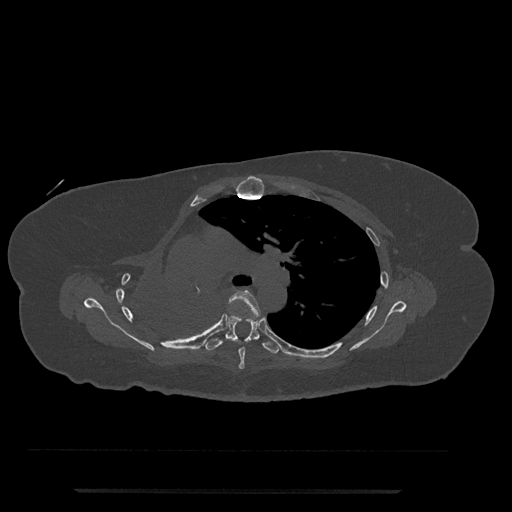
CT including the spine, one axial slice; position 516 of 797 along the scan axis; reconstruction kernel Br40s/3; 120 kVp; bone window (W 1800 / L 400 HU); 0.5 mm slice thickness; 512 × 512 image matrix, field of view 440 × 440 mm. Patient: female, 51 years. From the clinical record (not read from this slice): primary cancer: neuro.
Structures marked on this image (semi-automatically segmented with operator editing):
- T5 vertebra: bounding box [x1, y1, x2, y2] px = [196, 290, 264, 370]
- T6 vertebra: [205, 316, 280, 354]